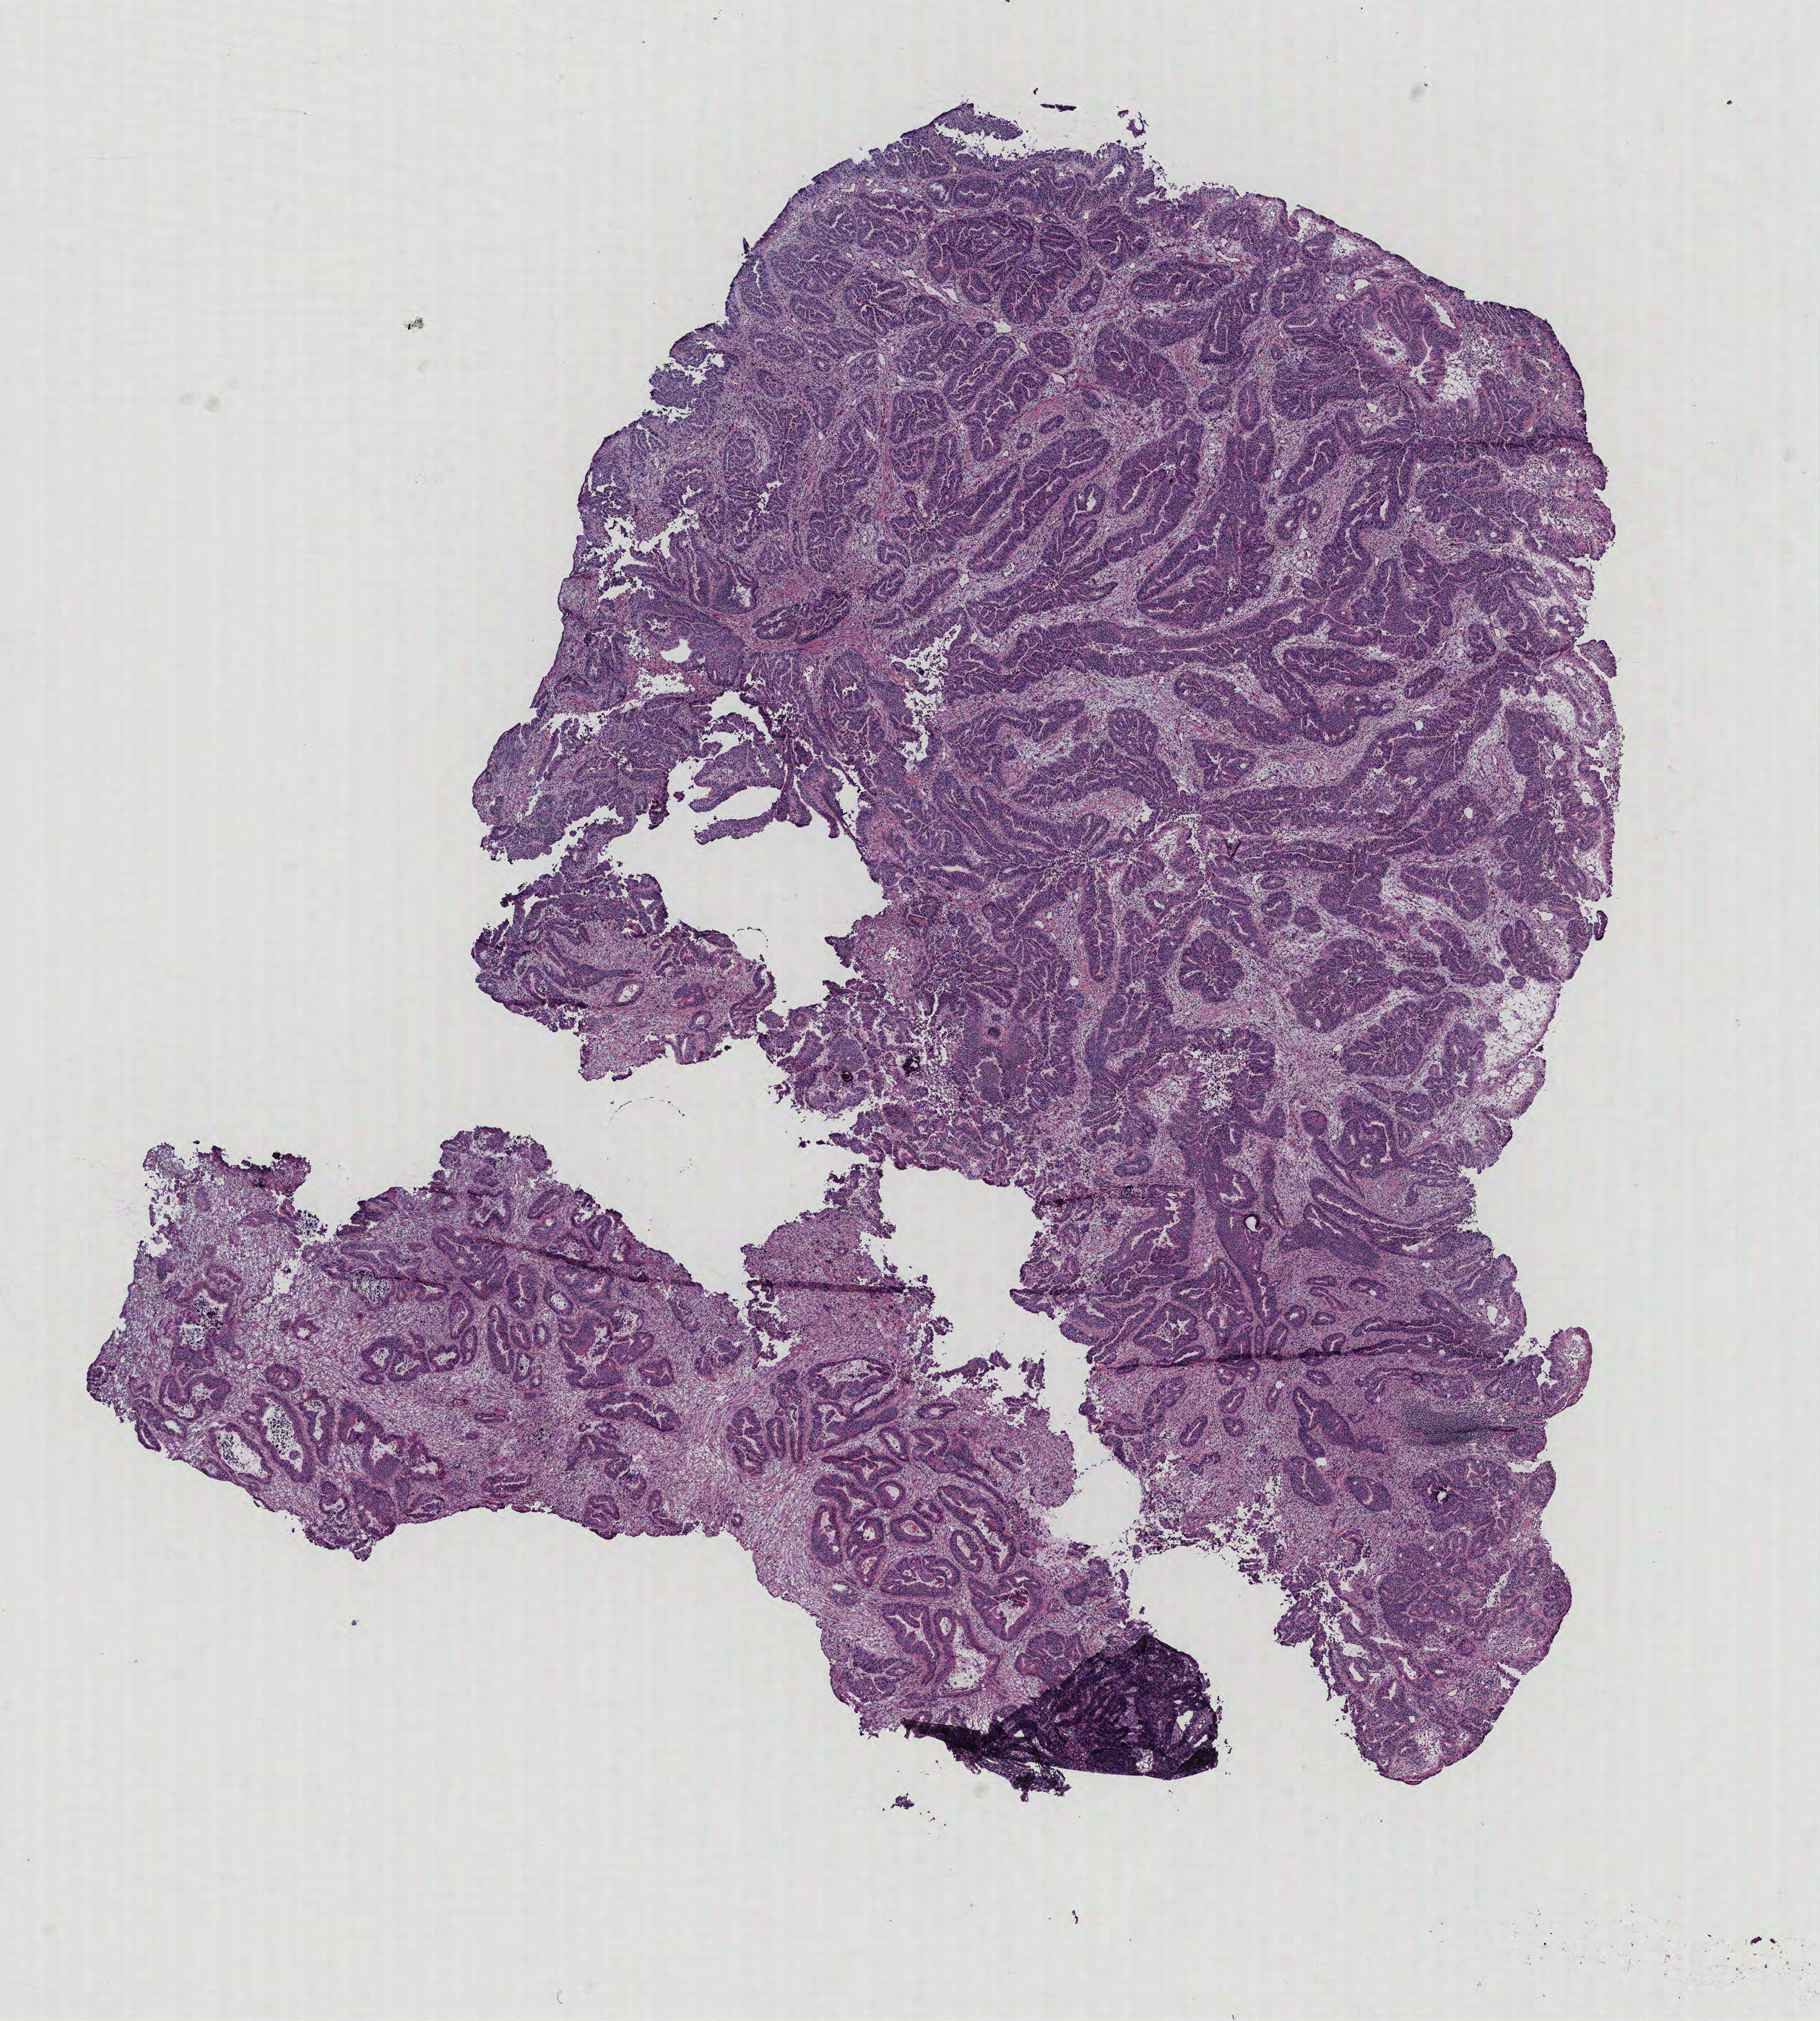
Whole-slide histology image, H&E-stained, low-resolution overview of the scanned area, about 10.1 x 11.2 mm (from a 40x scan), colon, tissue type not recorded. Patient sex: male.
• patient diagnosis: Adenocarcinoma, NOS